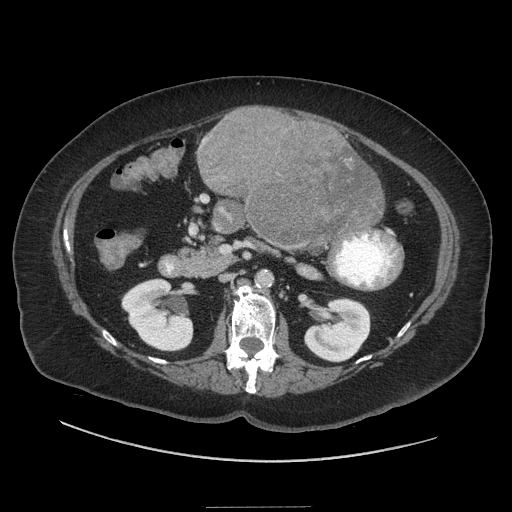
Contrast-enhanced abdominal CT (liver protocol), one axial slice. Position 1 of 81 along the scan axis. Reconstruction kernel STANDARD. 140 kVp. Soft-tissue window (W 400 / L 40 HU). 2.5 mm slice thickness. 512 × 512 image matrix. From the clinical record (not read from this slice): diagnosis: hepatocellular carcinoma (patient treated with transarterial chemoembolisation; whether this scan precedes or follows treatment is not stated here); TNM stage (as recorded): Stage-II; Child-Pugh class: A; tumour differentiation: moderately differentiated.
Outlined on this slice (semi-automatically segmented with operator editing):
- liver parenchyma outside the tumour (the mass and vessels are separate outlines, so this box may not span the whole liver): bounding box [x1, y1, x2, y2] px = [198, 118, 384, 236]
- mass: [196, 105, 383, 249]